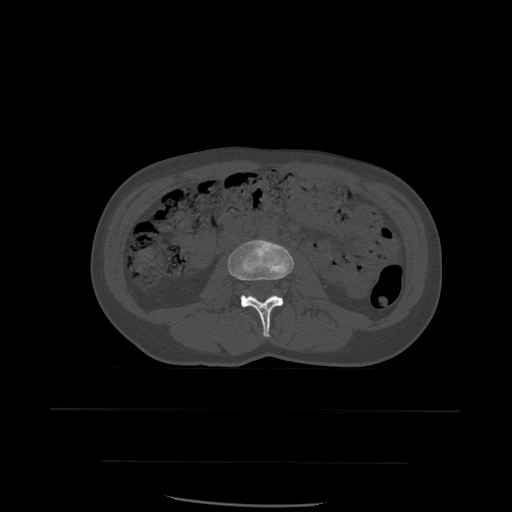
CT including the spine, one axial slice. Position 193 of 574 along the scan axis. Bone window (W 1800 / L 400 HU). 1.25 mm slice thickness. 512 × 512 image matrix, field of view 392 × 392 mm. Patient age 48 years. Case-level facts recorded for this patient, not image findings: primary cancer: lung.
Structures marked on this image (semi-automatic segmentation, software-assisted and operator-edited):
- L3 vertebra: bounding box [x1, y1, x2, y2] px = [228, 240, 294, 338]